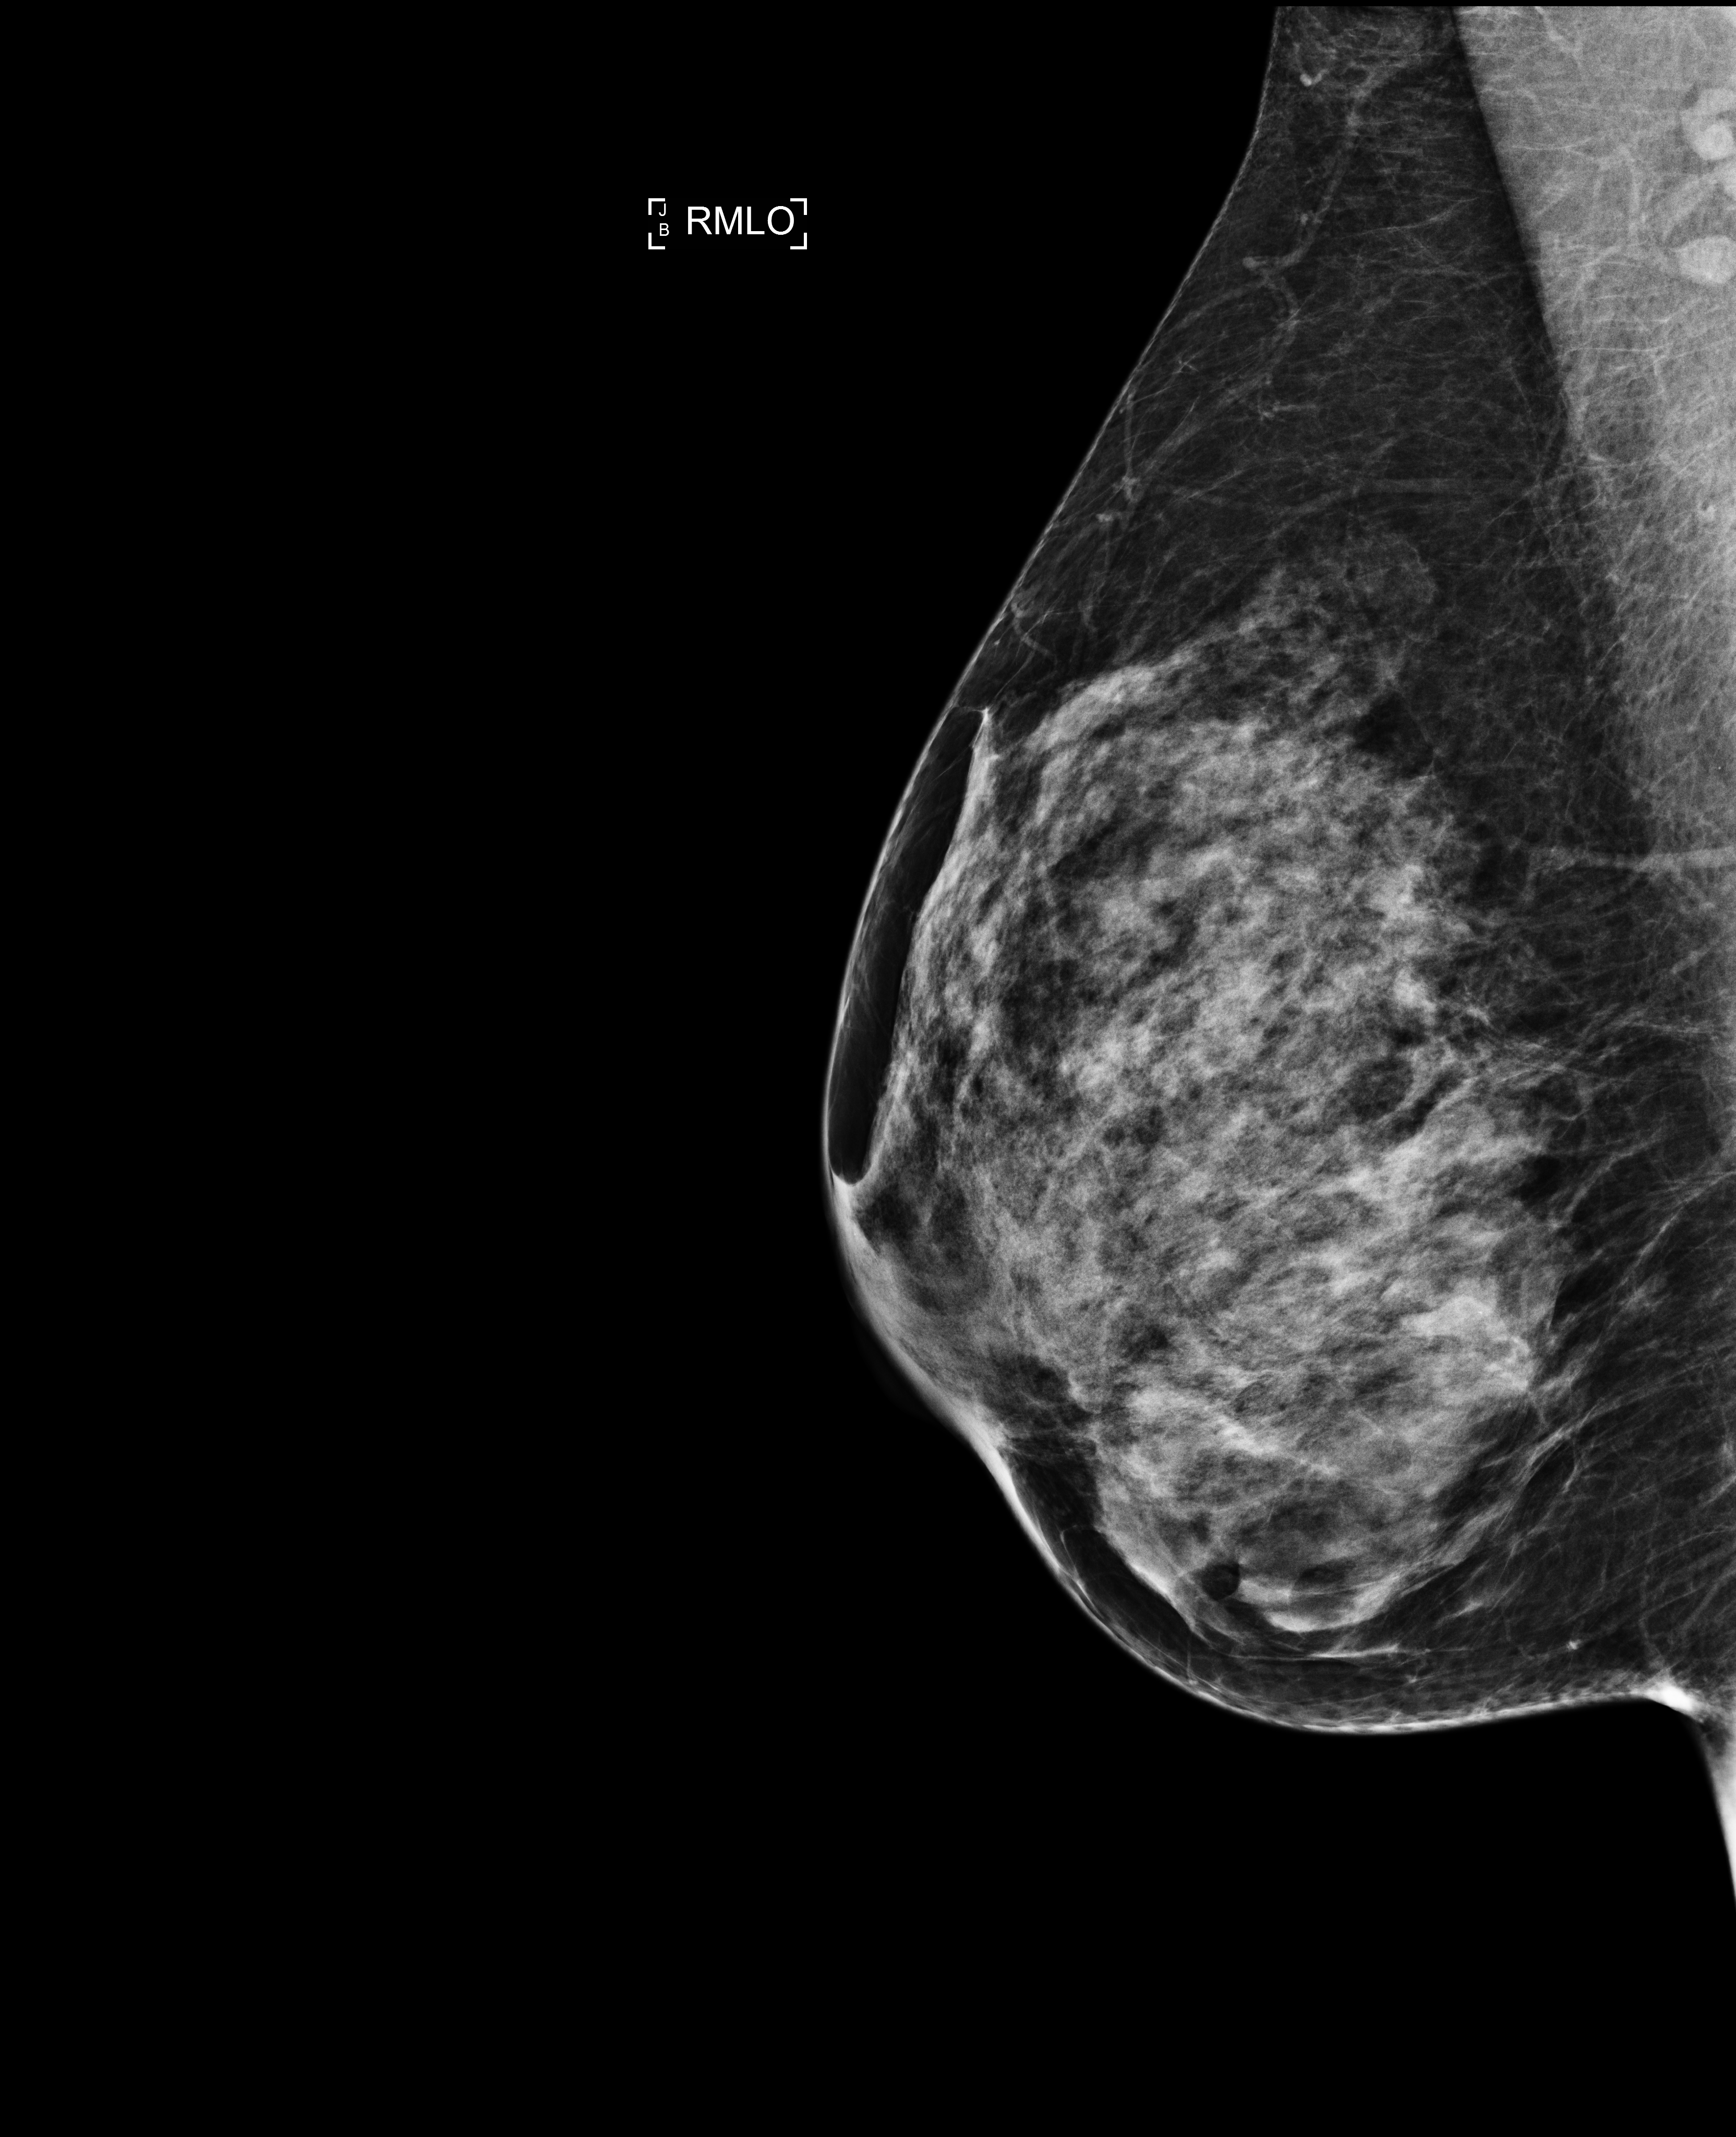
Screening examination, compressed breast thickness 58 mm, system: Selenia Dimensions. Patient aged 42 years (female).
Image type: full-field digital mammogram. Breast: right. Projection: medio-lateral oblique projection.